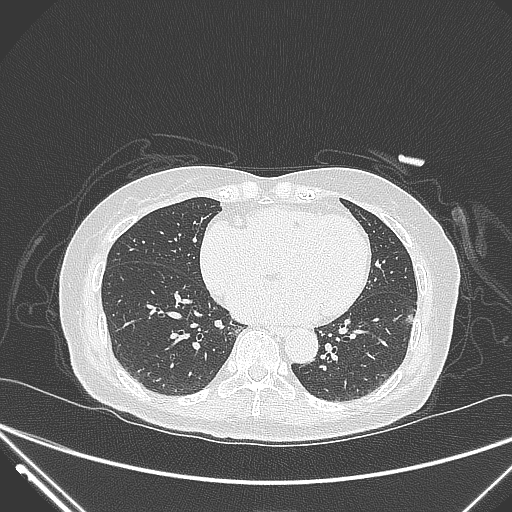
Chest CT, one axial slice. Position 119 of 310 along the scan axis. Lung window (W 1500 / L -600 HU). 512 × 512 image matrix, field of view 377 × 377 mm. Patient: female, 82 years. Case-level facts recorded for this patient, not image findings: clinical TNM (as recorded): T1c N0 M0; histopathological grade: G2.
Outlined on this slice (rectangle marked by the reading radiologist):
- lung tumour (recorded histology: adenocarcinoma): bounding box [x1, y1, x2, y2] px = [400, 310, 424, 334]